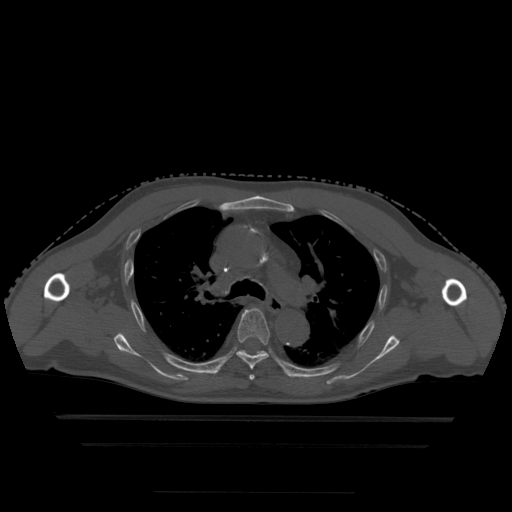
CT including the spine, one axial slice; slice 335 of 522 in the series (ordered by position); bone window (W 1800 / L 400 HU); 512 × 512 image matrix, field of view 436 × 436 mm. Patient age 68 years. Case-level facts recorded for this patient, not image findings: primary cancer: urothelial.
Outlined on this slice (semi-automatically segmented with operator editing):
- T4 vertebra: bounding box [x1, y1, x2, y2] px = [249, 375, 255, 381]
- T5 vertebra: [237, 309, 270, 370]
- T6 vertebra: [239, 350, 267, 355]